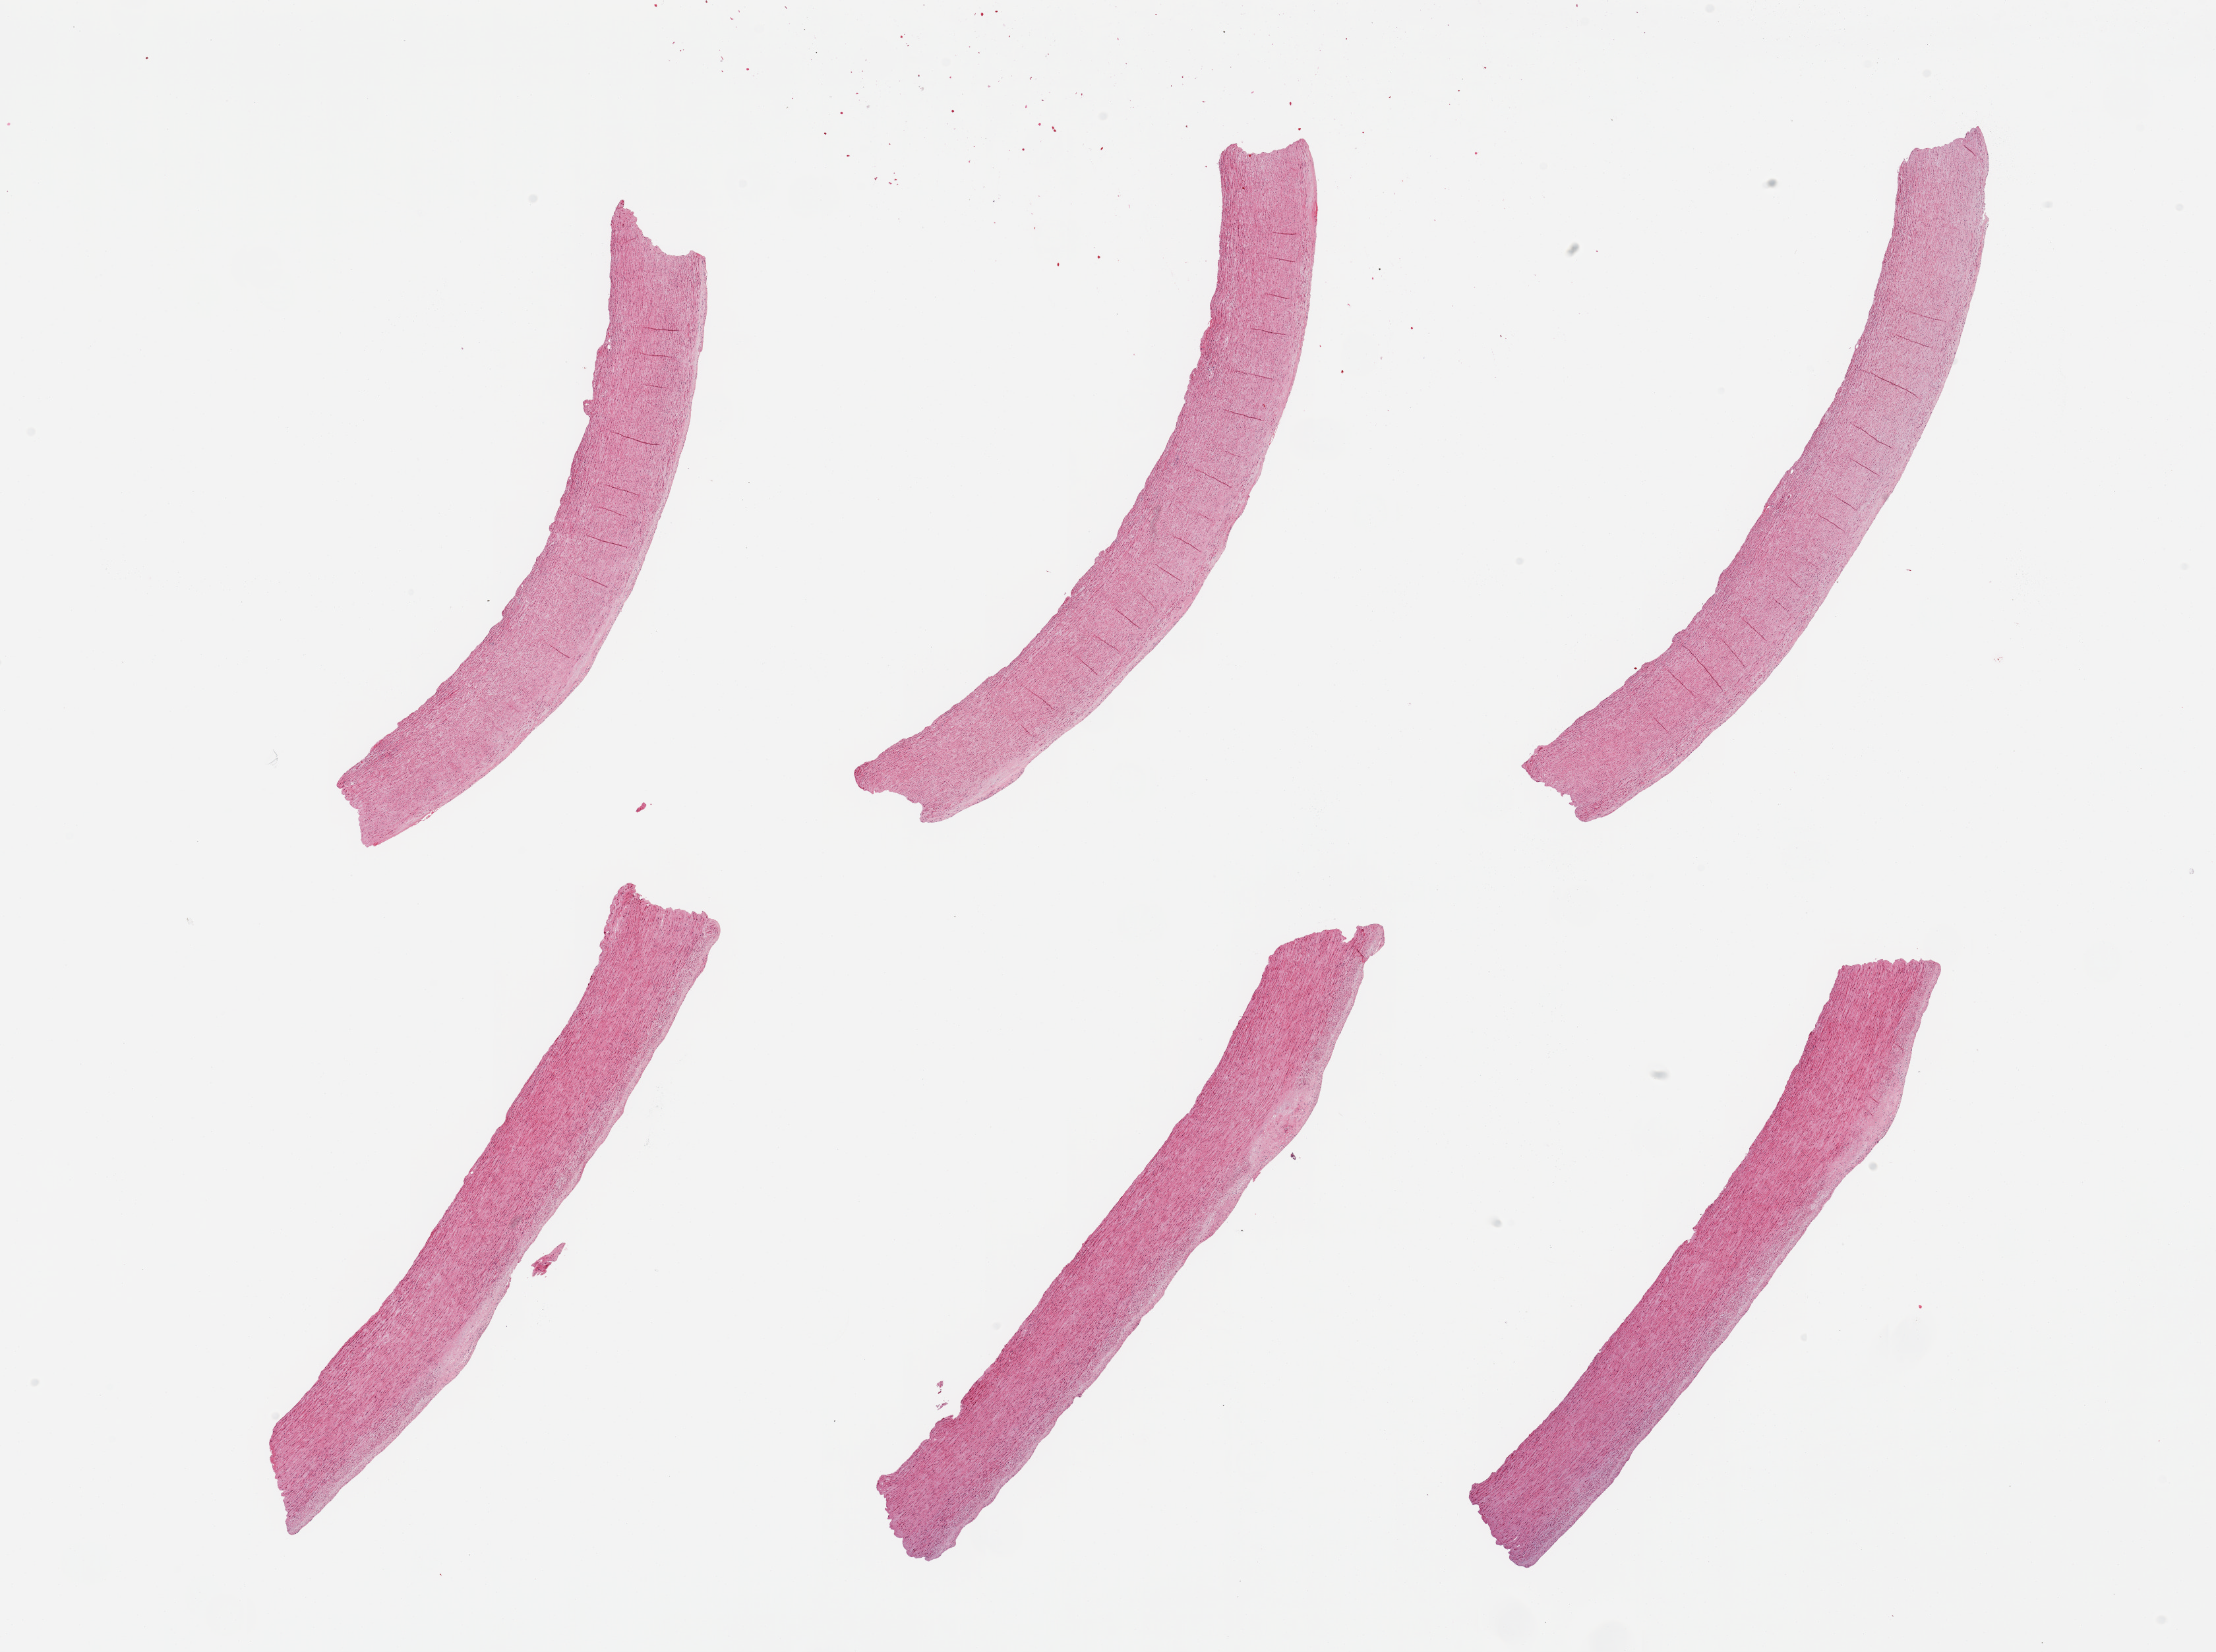
Digitized hematoxylin and eosin (H&E)-stained section, whole scanned area (about 26.6 x 19.8 mm) shown as a low-resolution overview. PAXgene-fixed paraffin-embedded (PFPE) section. Section of aorta (target tissue). Tissue donor sample. Male donor.
- reviewer comment on this tissue sample: 6 pieces, atherosis up to ~0.3mm